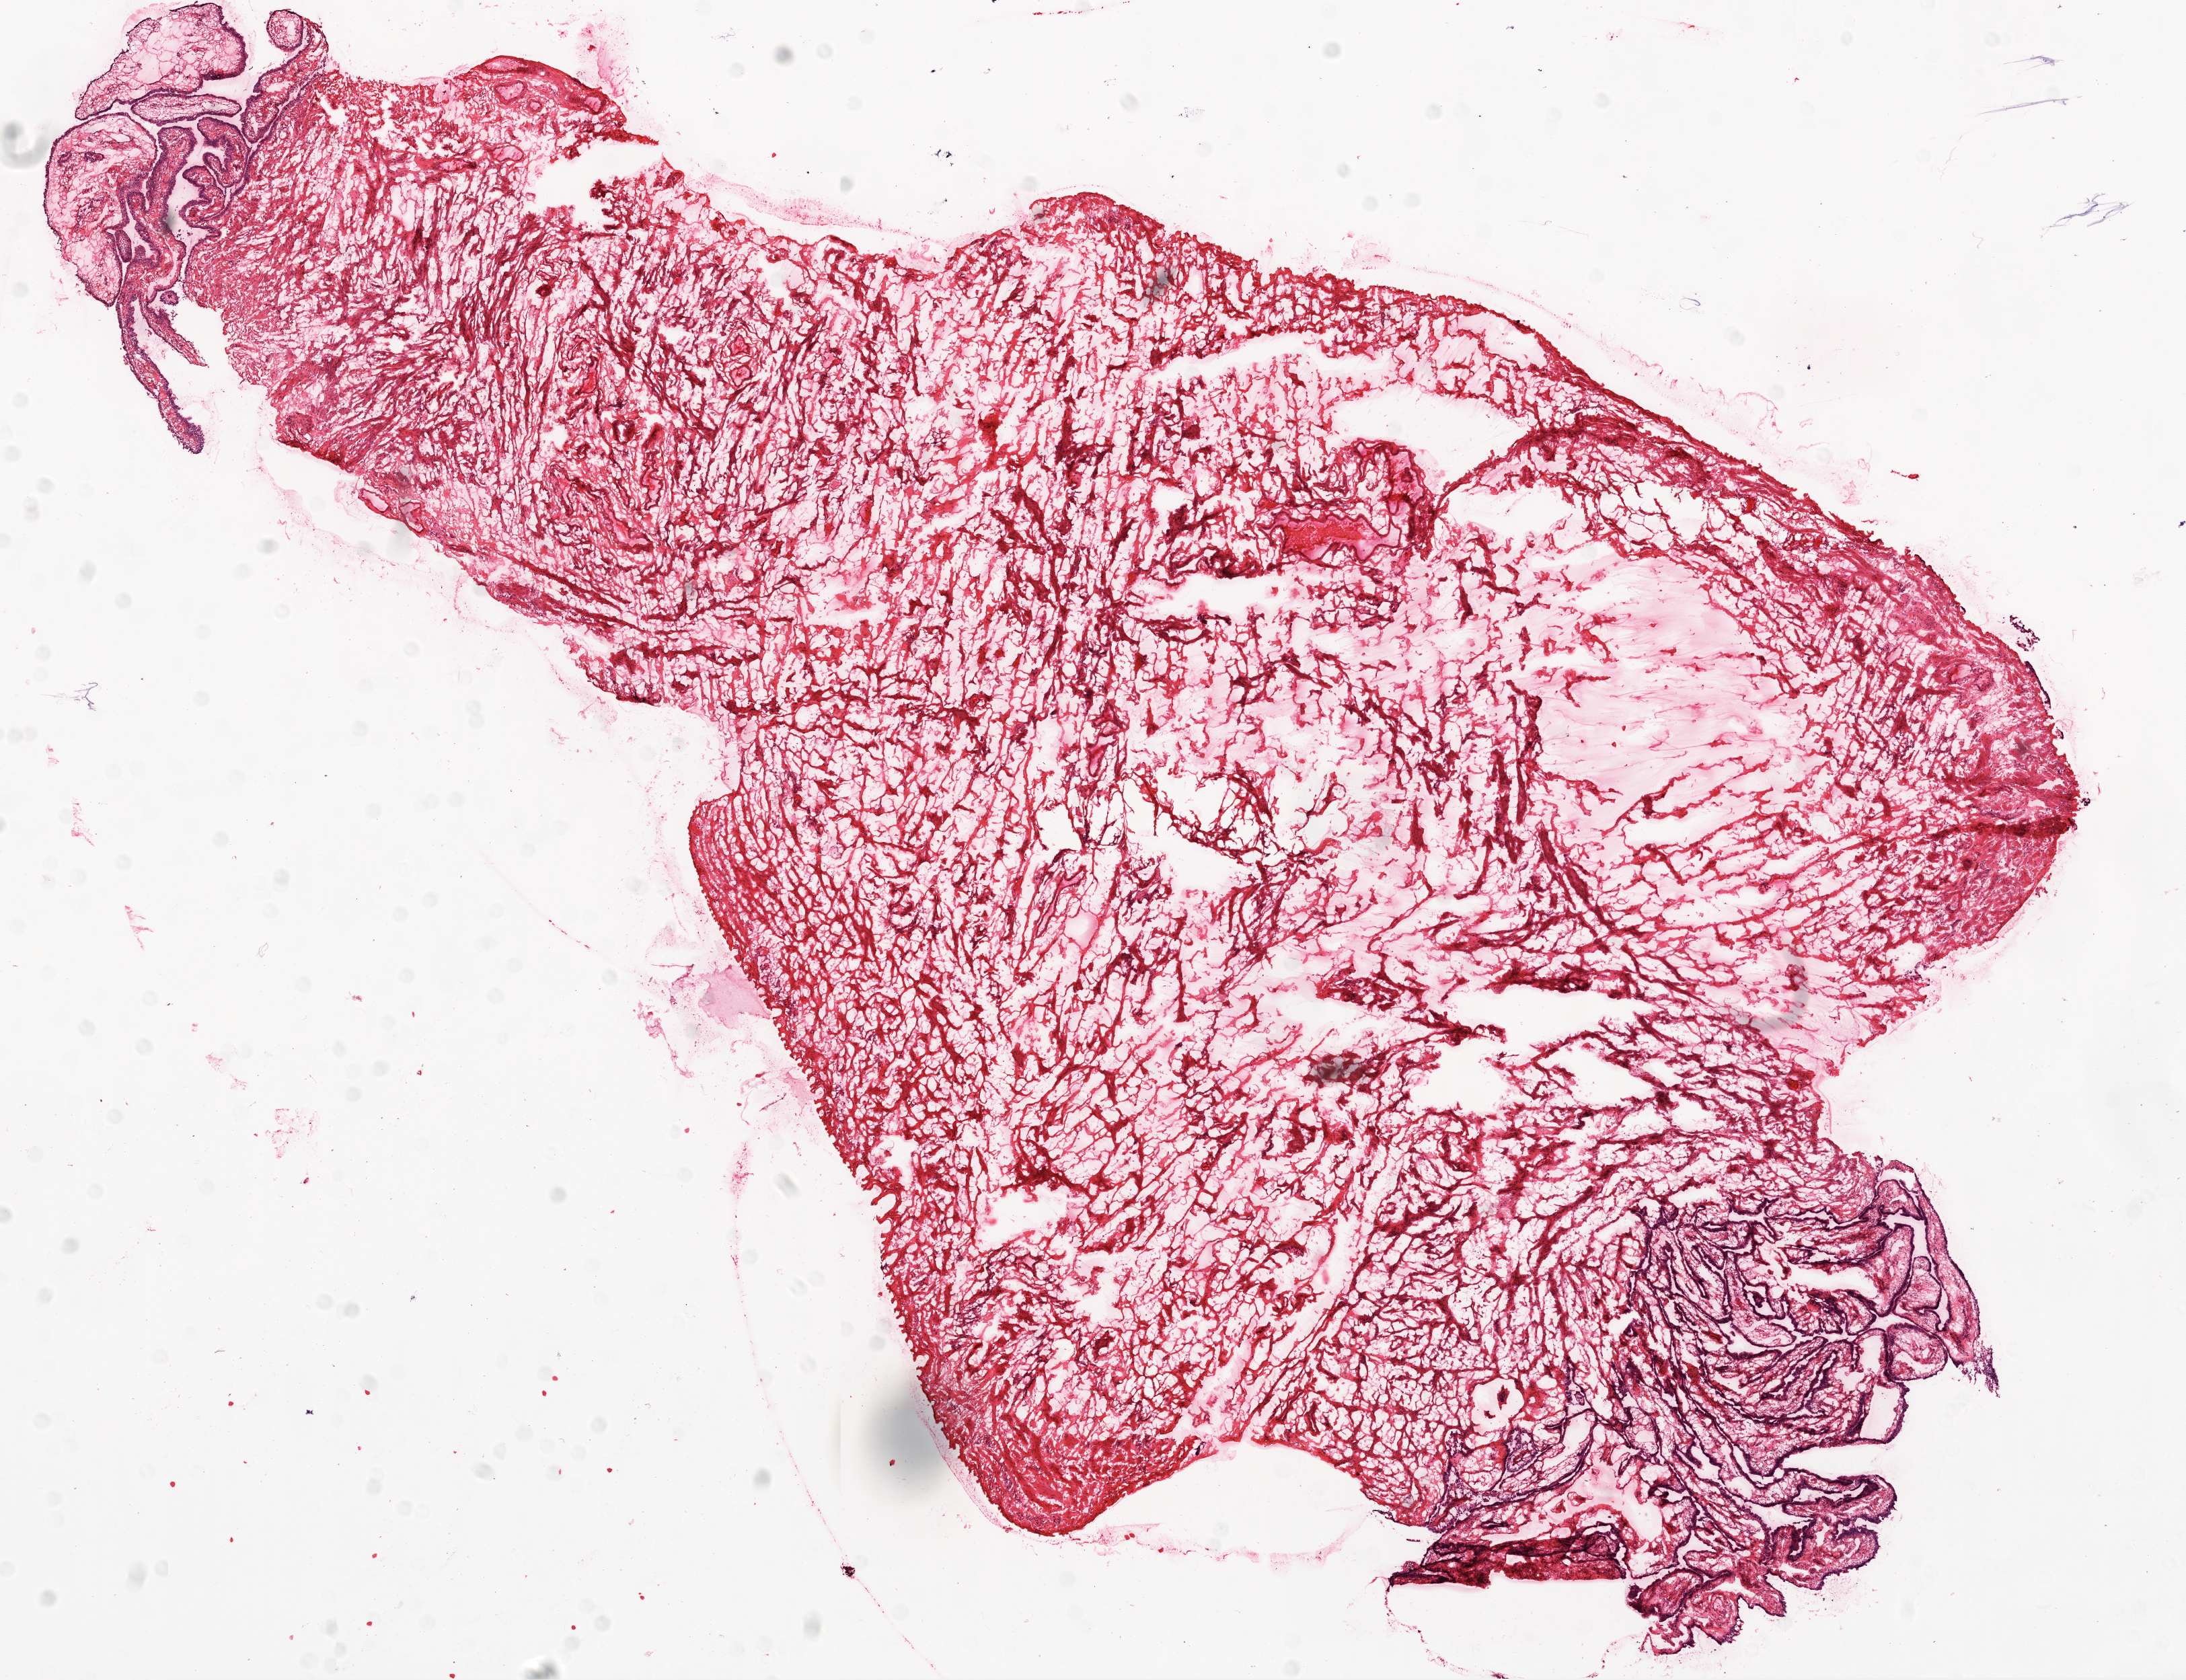
H&E whole-slide image — a low-resolution overview of the entire scanned area, about 13.0 x 10.0 mm (acquisition: 20x scan), frozen section from the top of the tissue portion, ovary, solid tissue normal (non-tumour tissue) sample. Patient: female, age at initial diagnosis 53 years.
This section: solid tissue normal sample (biorepository sample class). Patient diagnosis: Serous cystadenocarcinoma, NOS.